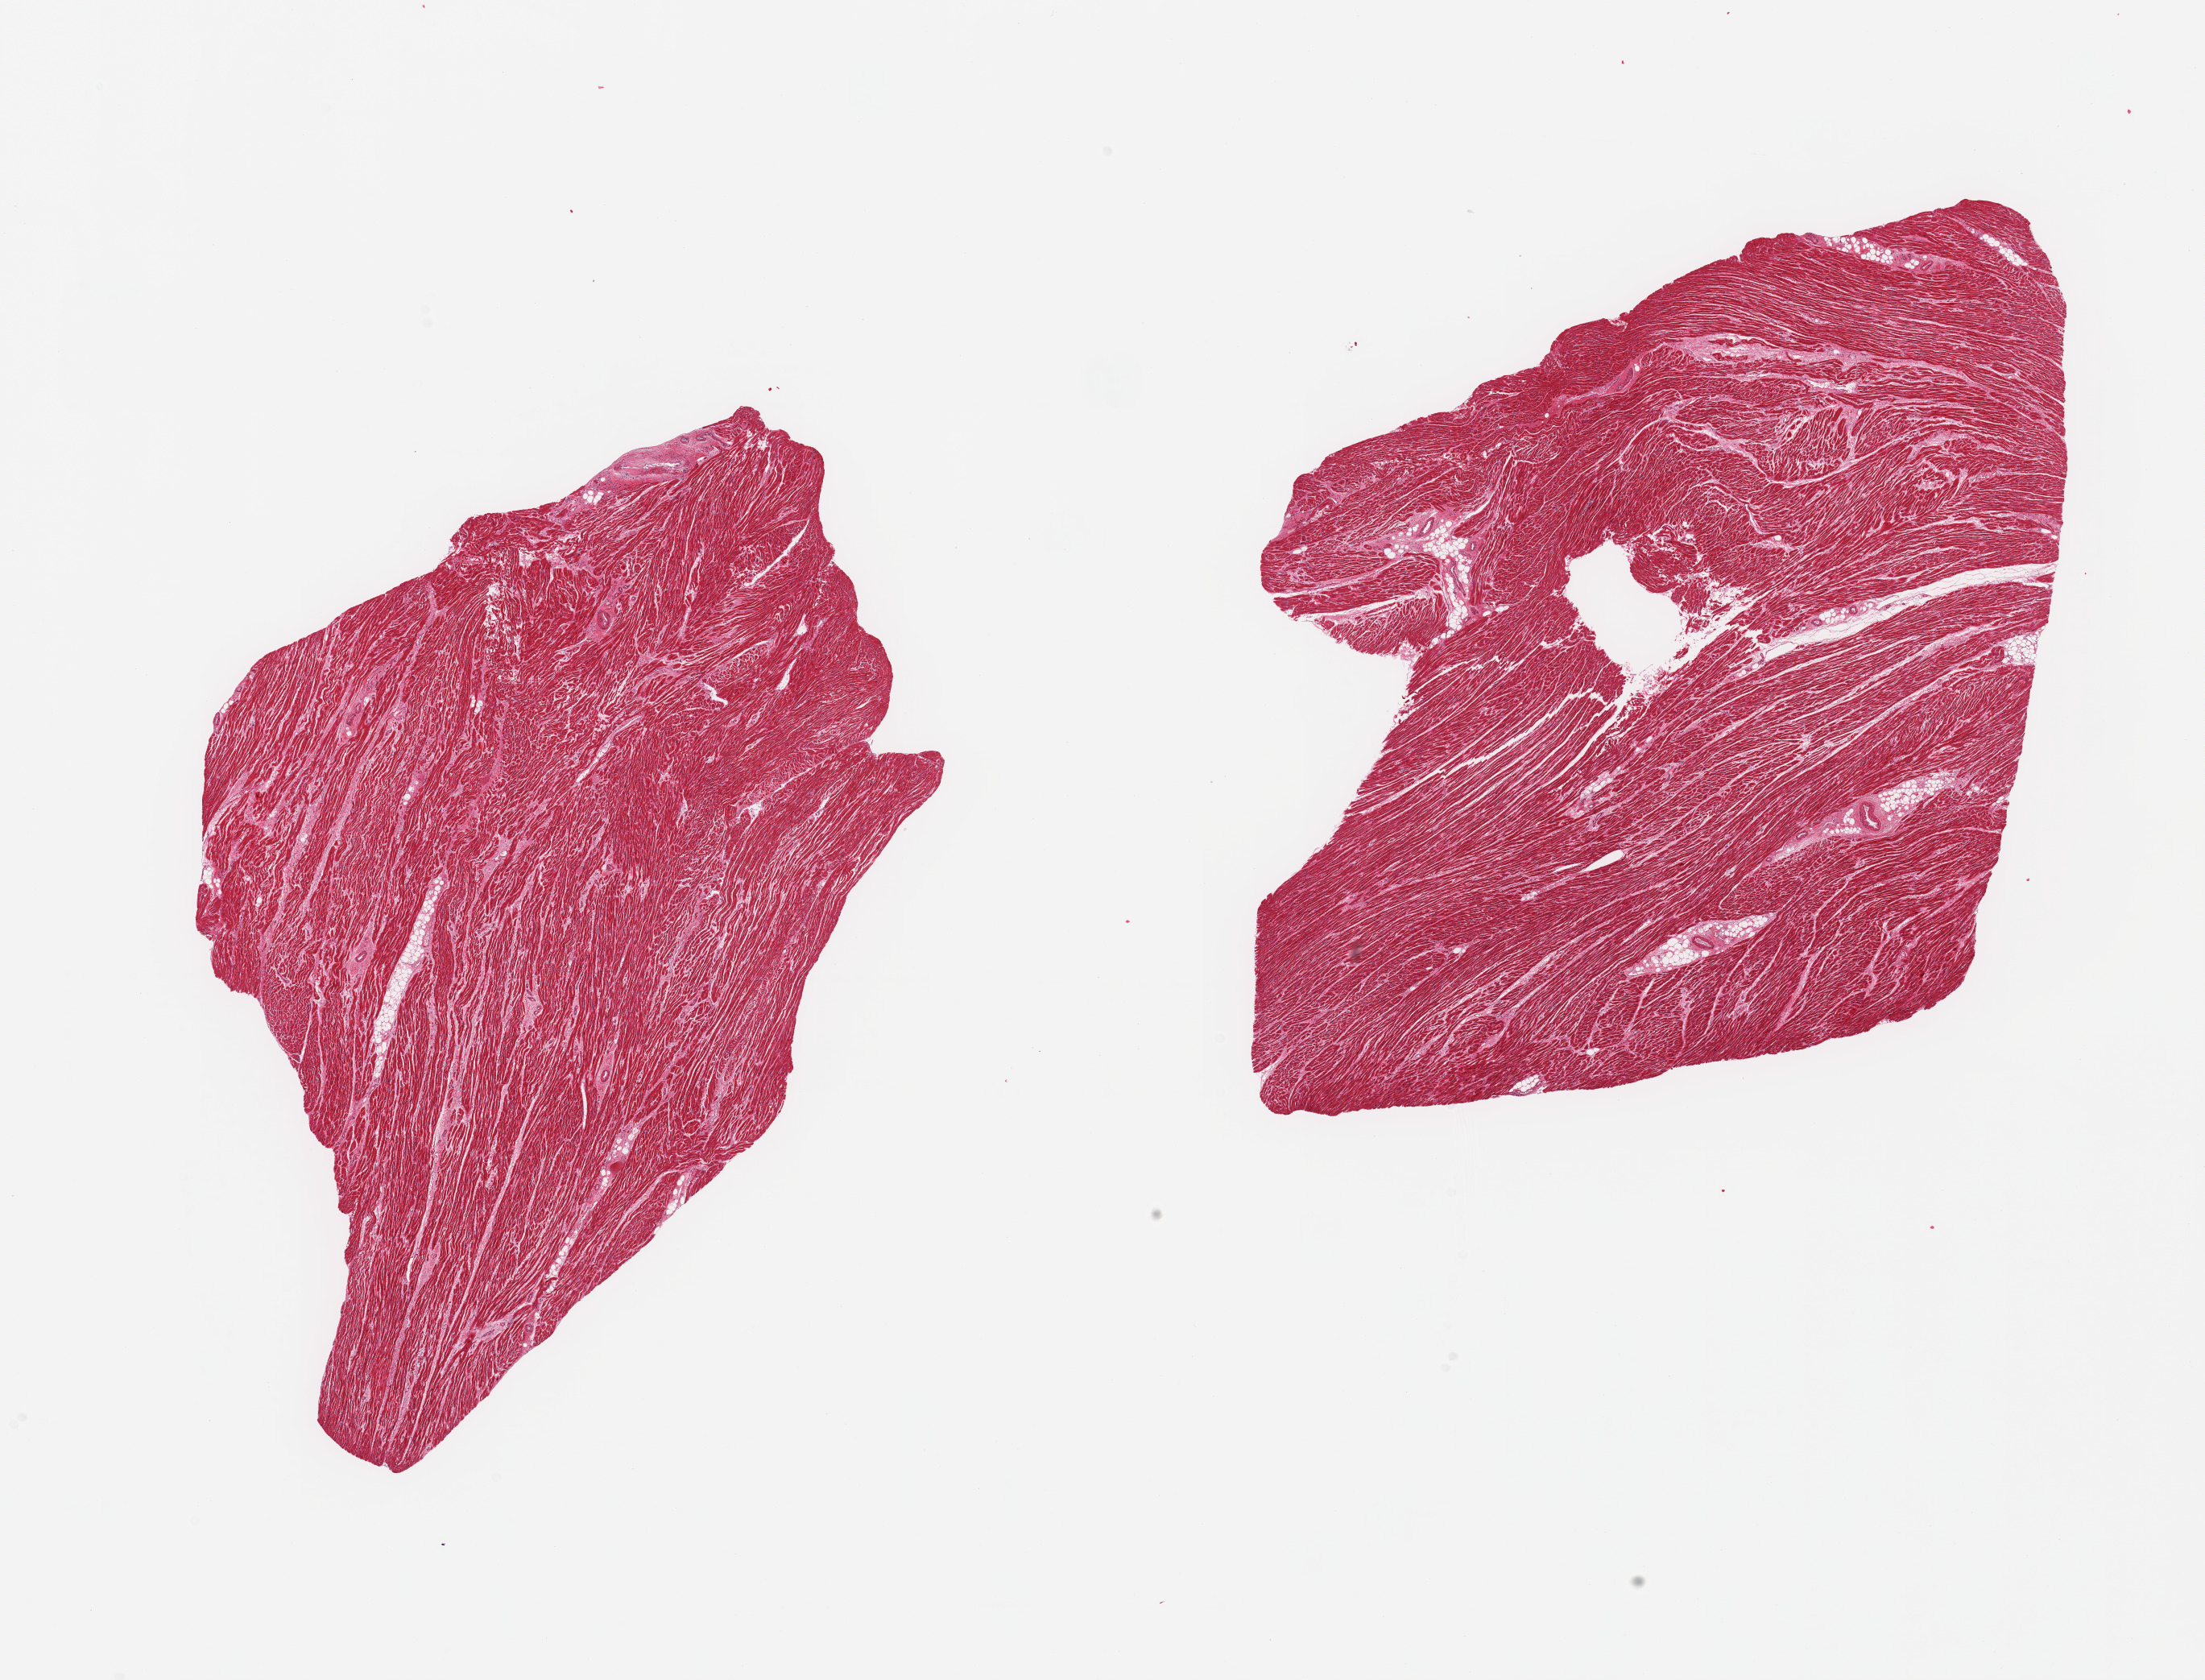
Whole-slide image, H&E stain, brightfield, shown as a low-resolution overview of the whole scanned area (about 21.7 x 16.5 mm); PAXgene-fixed, paraffin-embedded tissue; section of heart (target tissue); donor tissue sample. Male donor.
Reviewer comment on this tissue sample: 2 pieces; some interstitial fibrosis and focal fatty degeneration.